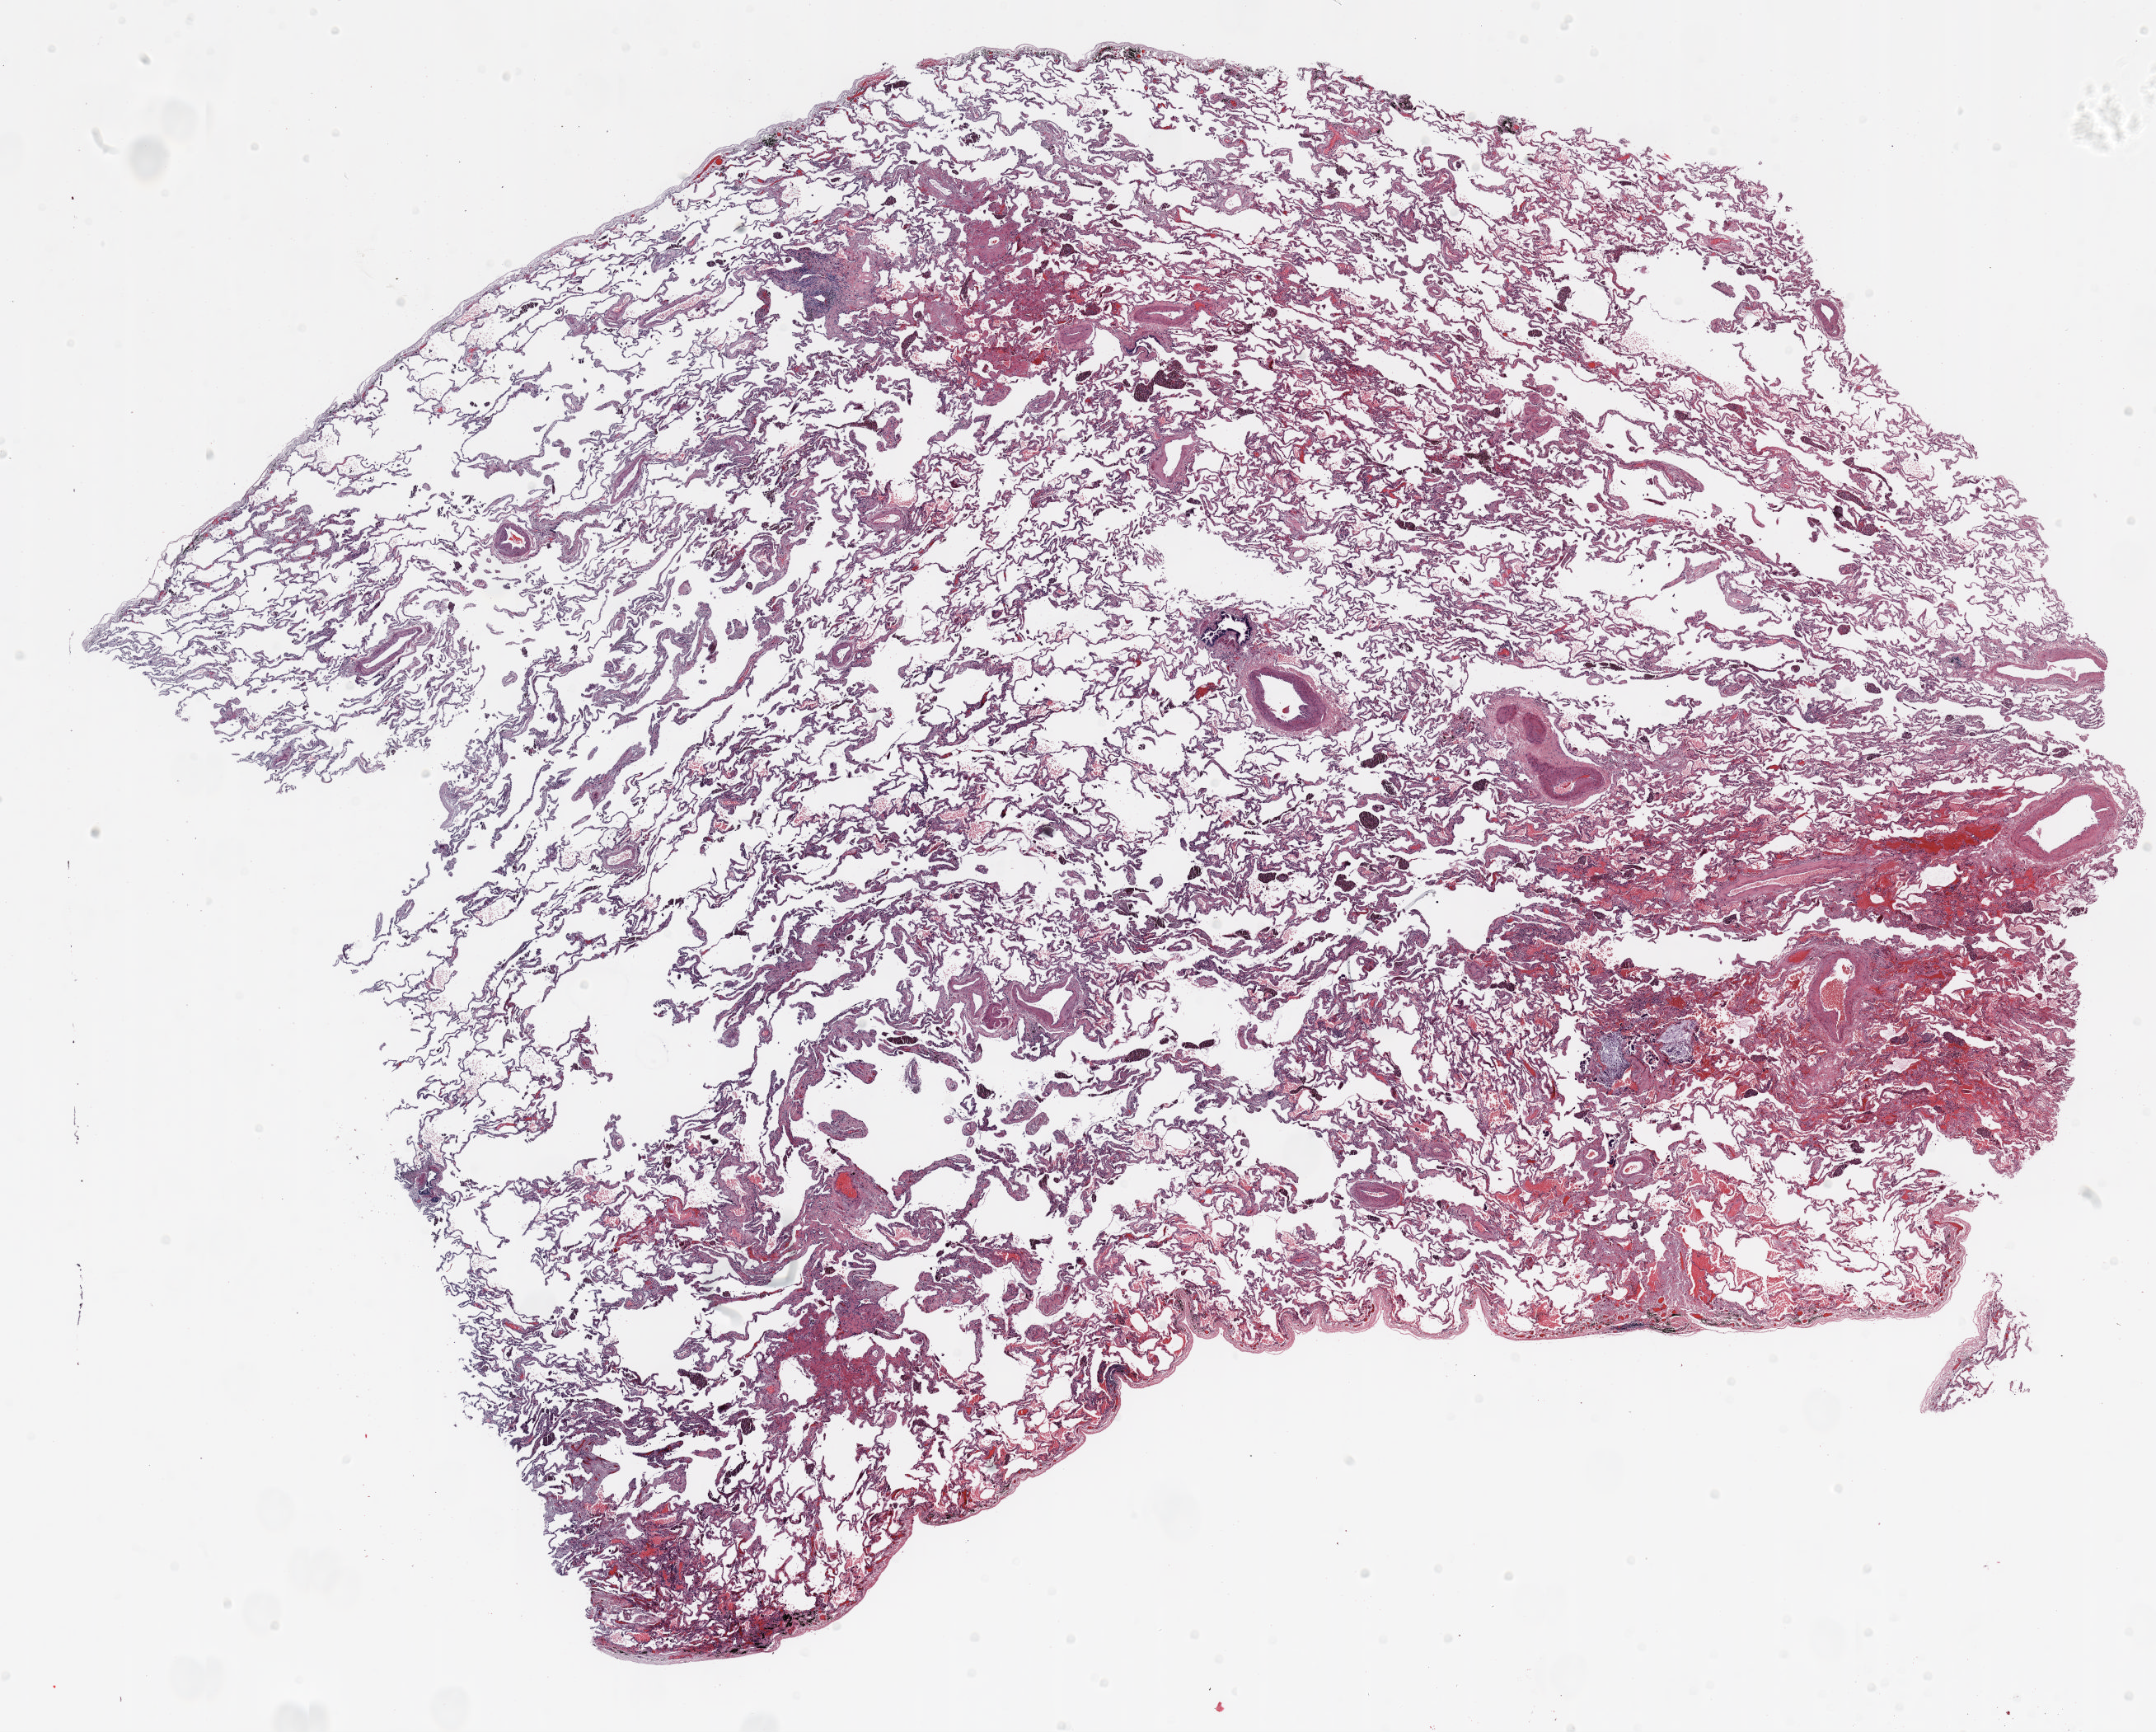
H&E-stained whole-slide image — shown as a low-resolution overview of the whole scanned area (about 21.0 x 16.9 mm). FFPE section. Lung tissue. Female, age 72 at enrolment. Current smoker at enrolment.
Participant's lung-cancer diagnosis: Non-small cell carcinoma (ICD-O-3 8046/3).